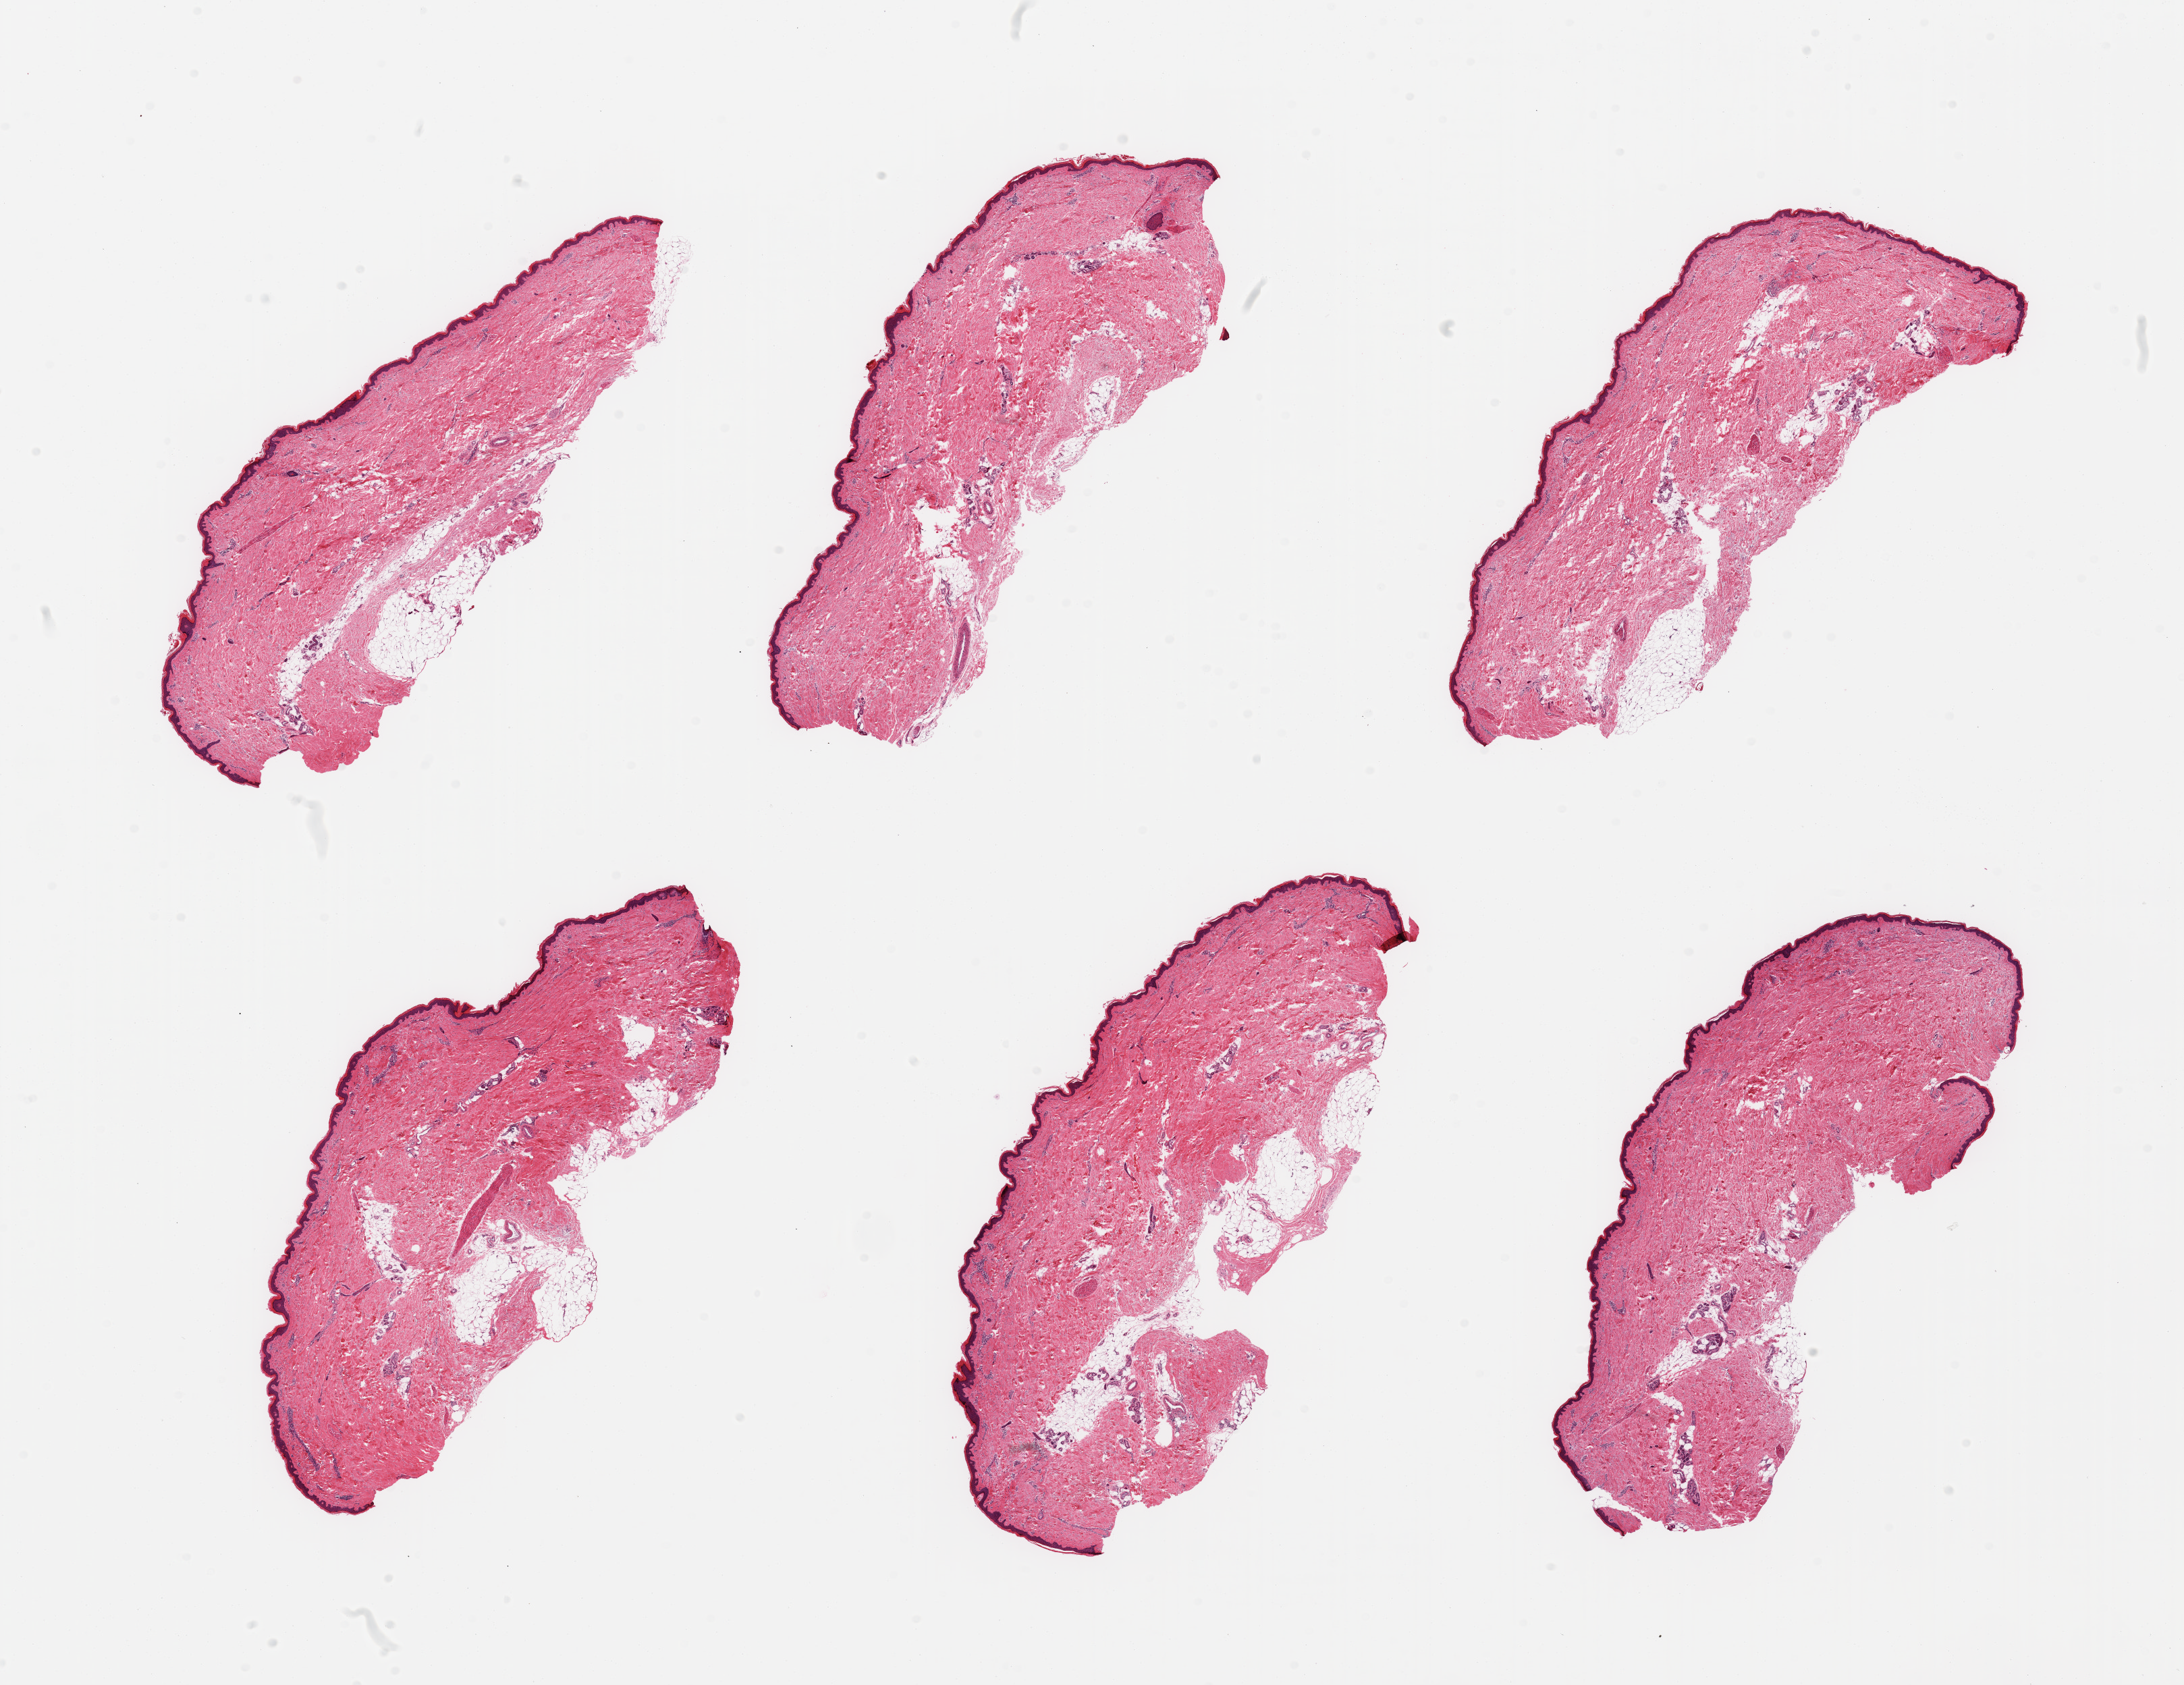
Whole-slide image, H&E stain — whole scanned area (about 25.6 x 19.7 mm) shown as a low-resolution overview; PAXgene-fixed paraffin-embedded (PFPE) section; sampled site (target tissue): skin of lower leg; tissue donor sample. Donor sex: female.
* pathologist's review note for this sample: 6 pieces, moderate dermal fat; squamous epithelium is ~405-50 microns